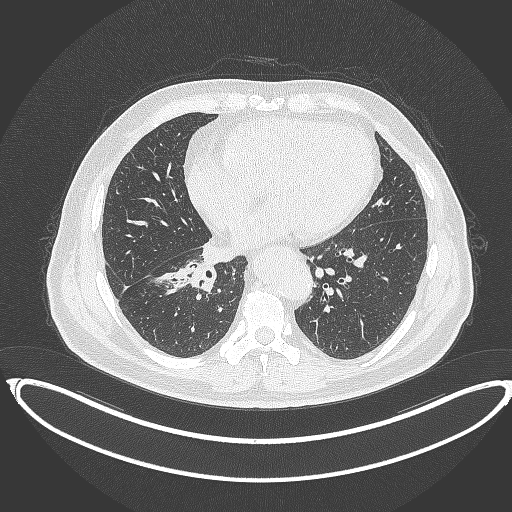
Chest CT, one axial slice. Position 161 of 387 along the scan axis. Lung window (W 1500 / L -600 HU). 1 mm slice thickness. 512 × 512 image matrix, field of view 448 × 448 mm. Patient: male, 61 years. From the clinical record (not read from this slice): clinical TNM (as recorded): T1b N1 M0.
Annotated regions visible in this slice (bounding box drawn by a radiologist):
- lung tumour (recorded histology: squamous cell carcinoma): bounding box (x1, y1, x2, y2) in pixels: (178, 257, 217, 294)